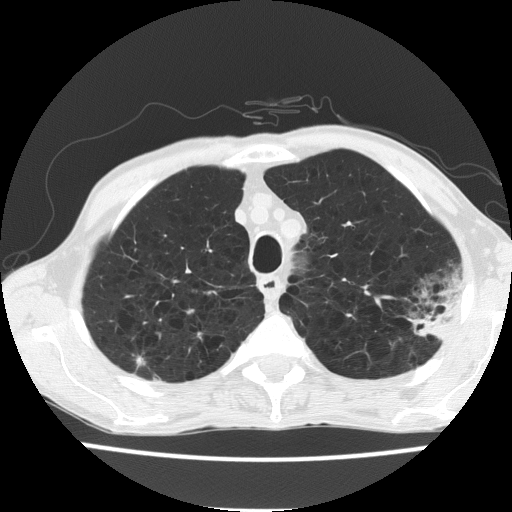
Chest CT (low-dose screening protocol), one axial image. First (baseline) screen. Lung window (W 1500 / L -600 HU). 2 mm slice thickness. Male participant, aged 60 years at enrolment. Current smoker at enrolment.
Lesion marked by an expert reader, bounding box [x1, y1, x2, y2] px = [394, 273, 464, 345]. No non-calcified nodule or mass ≥4 mm was recorded by the screening reader at this exam. Later outcome: lung cancer diagnosed 490 days after this screen — bronchiolo-alveolar carcinoma, mucinous, left upper lobe, stage IV (AJCC 6th edition).